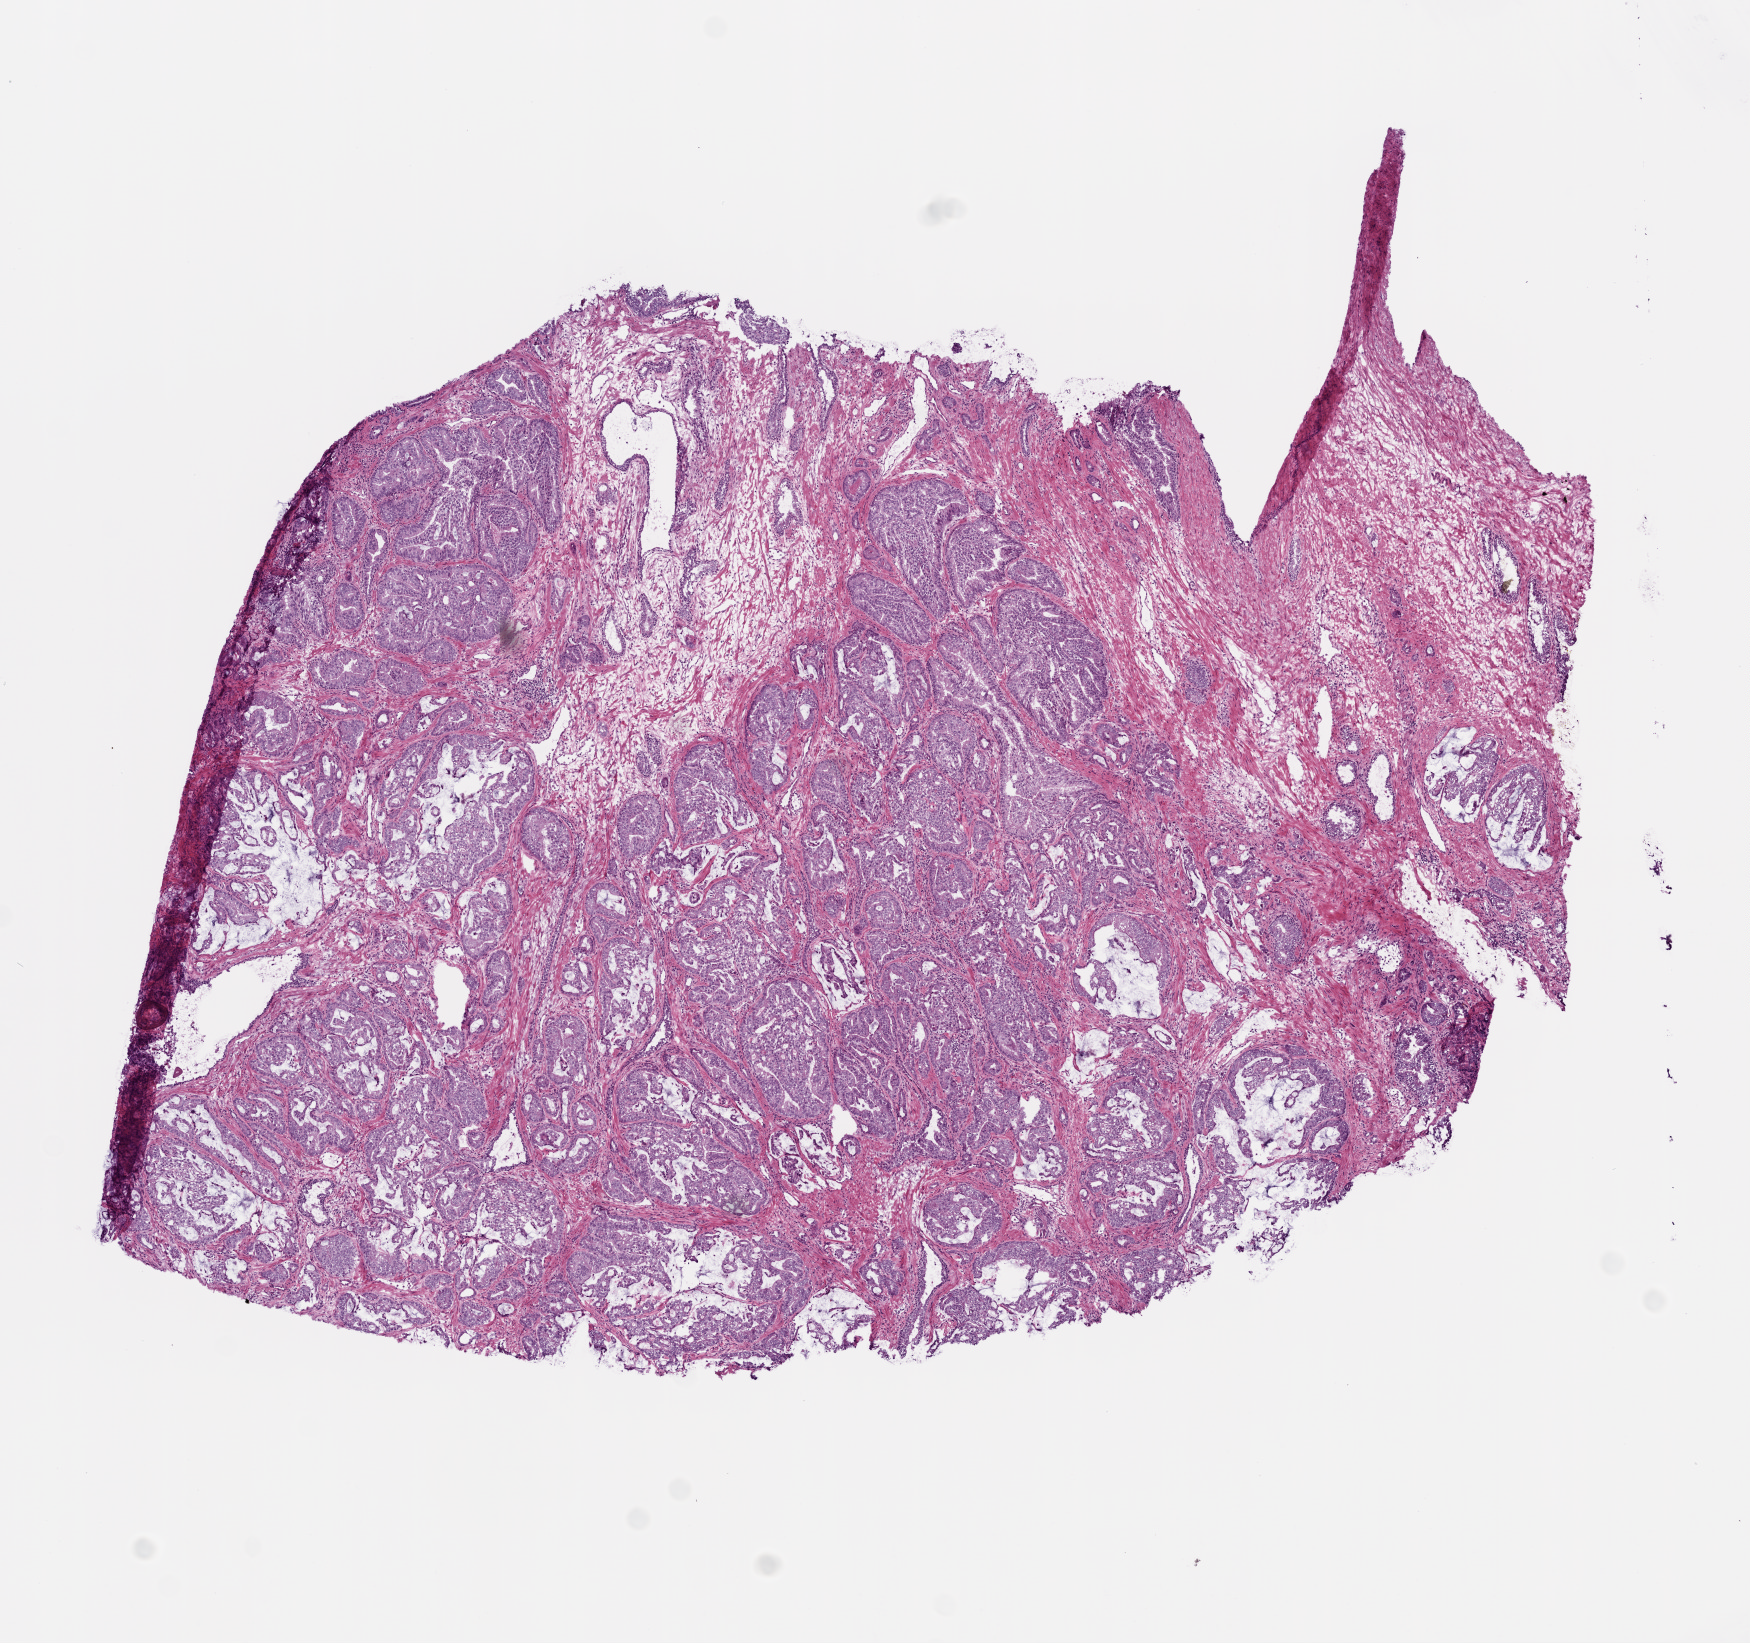
Whole-slide histology image, H&E, shown as a low-resolution overview of the whole scanned area (about 7.0 x 6.6 mm). Frozen section from the top of the tissue portion. Sample: primary tumour, prostate. Male, age 64 years at initial diagnosis. Gleason score: 7 (4+3). Slide review estimates, as recorded: tumour cells 65%, tumour nuclei 70%, normal cells 15%, stromal cells 20%, necrosis 0%. Infiltration values recorded for this section: lymphocyte infiltration 0%, monocyte infiltration 0%, neutrophil infiltration 0%.
Histologic diagnosis: Acinar cell carcinoma. Laterality: bilateral. Lymph nodes positive (case pathology): 0 of 3 examined.